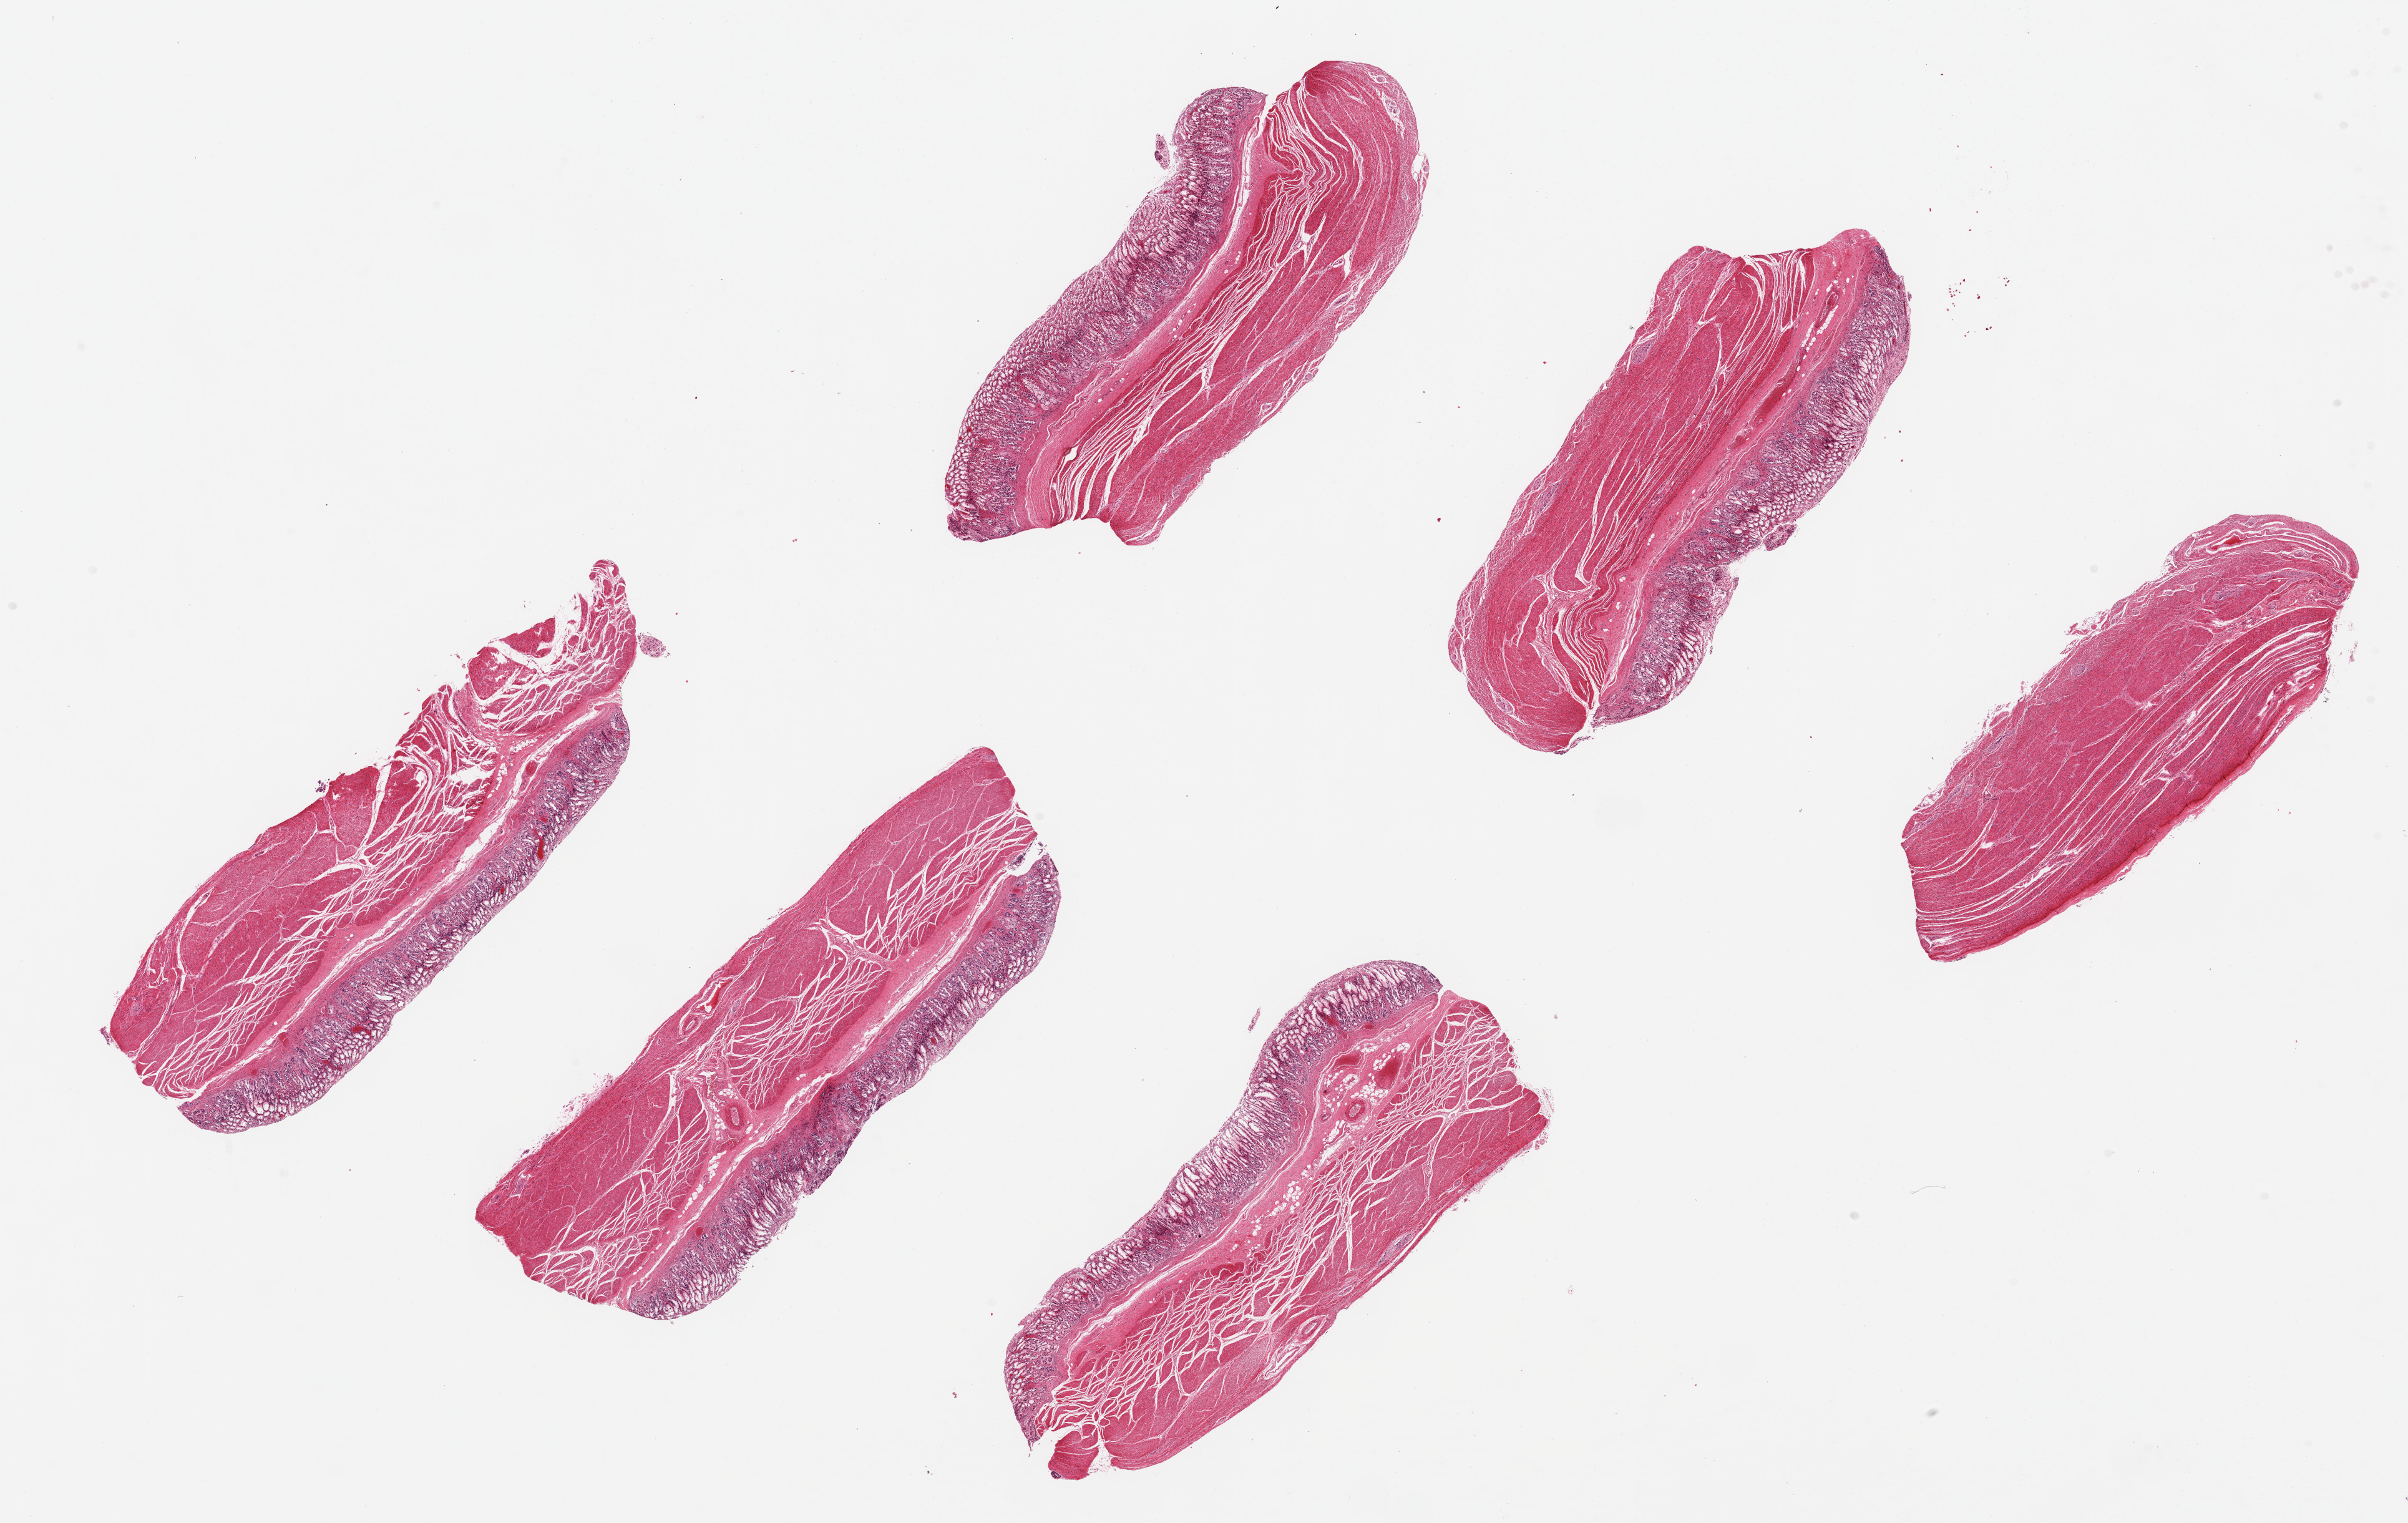
Whole-slide image, hematoxylin and eosin (H&E) stain, low-resolution overview of the scanned area, about 30.5 x 19.3 mm; PAXgene-fixed, paraffin-embedded tissue; section of stomach (target tissue); tissue donor sample. Donor: male.
Pathologist's review note for this sample: 6 pieces, ~8x2.5mm. Mucosal glands badly autolyzed; mucosa is ~25-30% of thickenss.